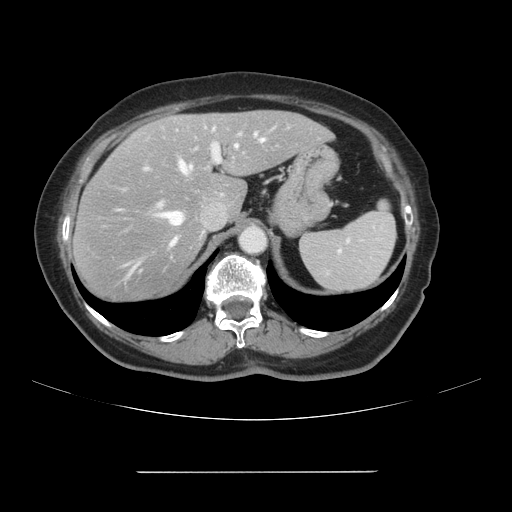
Contrast-enhanced abdominal CT, one axial slice; slice 74 of 111 in the series (ordered by position); 120 kVp; intravenous contrast given; soft-tissue window (W 400 / L 40 HU); 2.5 mm slice thickness; 512 × 512 image matrix. Female patient, age 74 years. Case-level facts recorded for this patient, not image findings: diagnosis: colorectal cancer liver metastases, imaged before liver resection; multiple liver metastases: yes; largest metastasis: 1.1 cm; disease in both lobes: yes.
Structures marked on this image (outlined manually by an expert reader):
- hepatic veins: bounding box [x1, y1, x2, y2] px = [121, 133, 265, 281]
- liver: [74, 111, 332, 303]
- planned liver remnant (the part of the liver to remain after resection): [155, 111, 331, 217]
- portal vein (with intrahepatic branches): [145, 129, 240, 207]